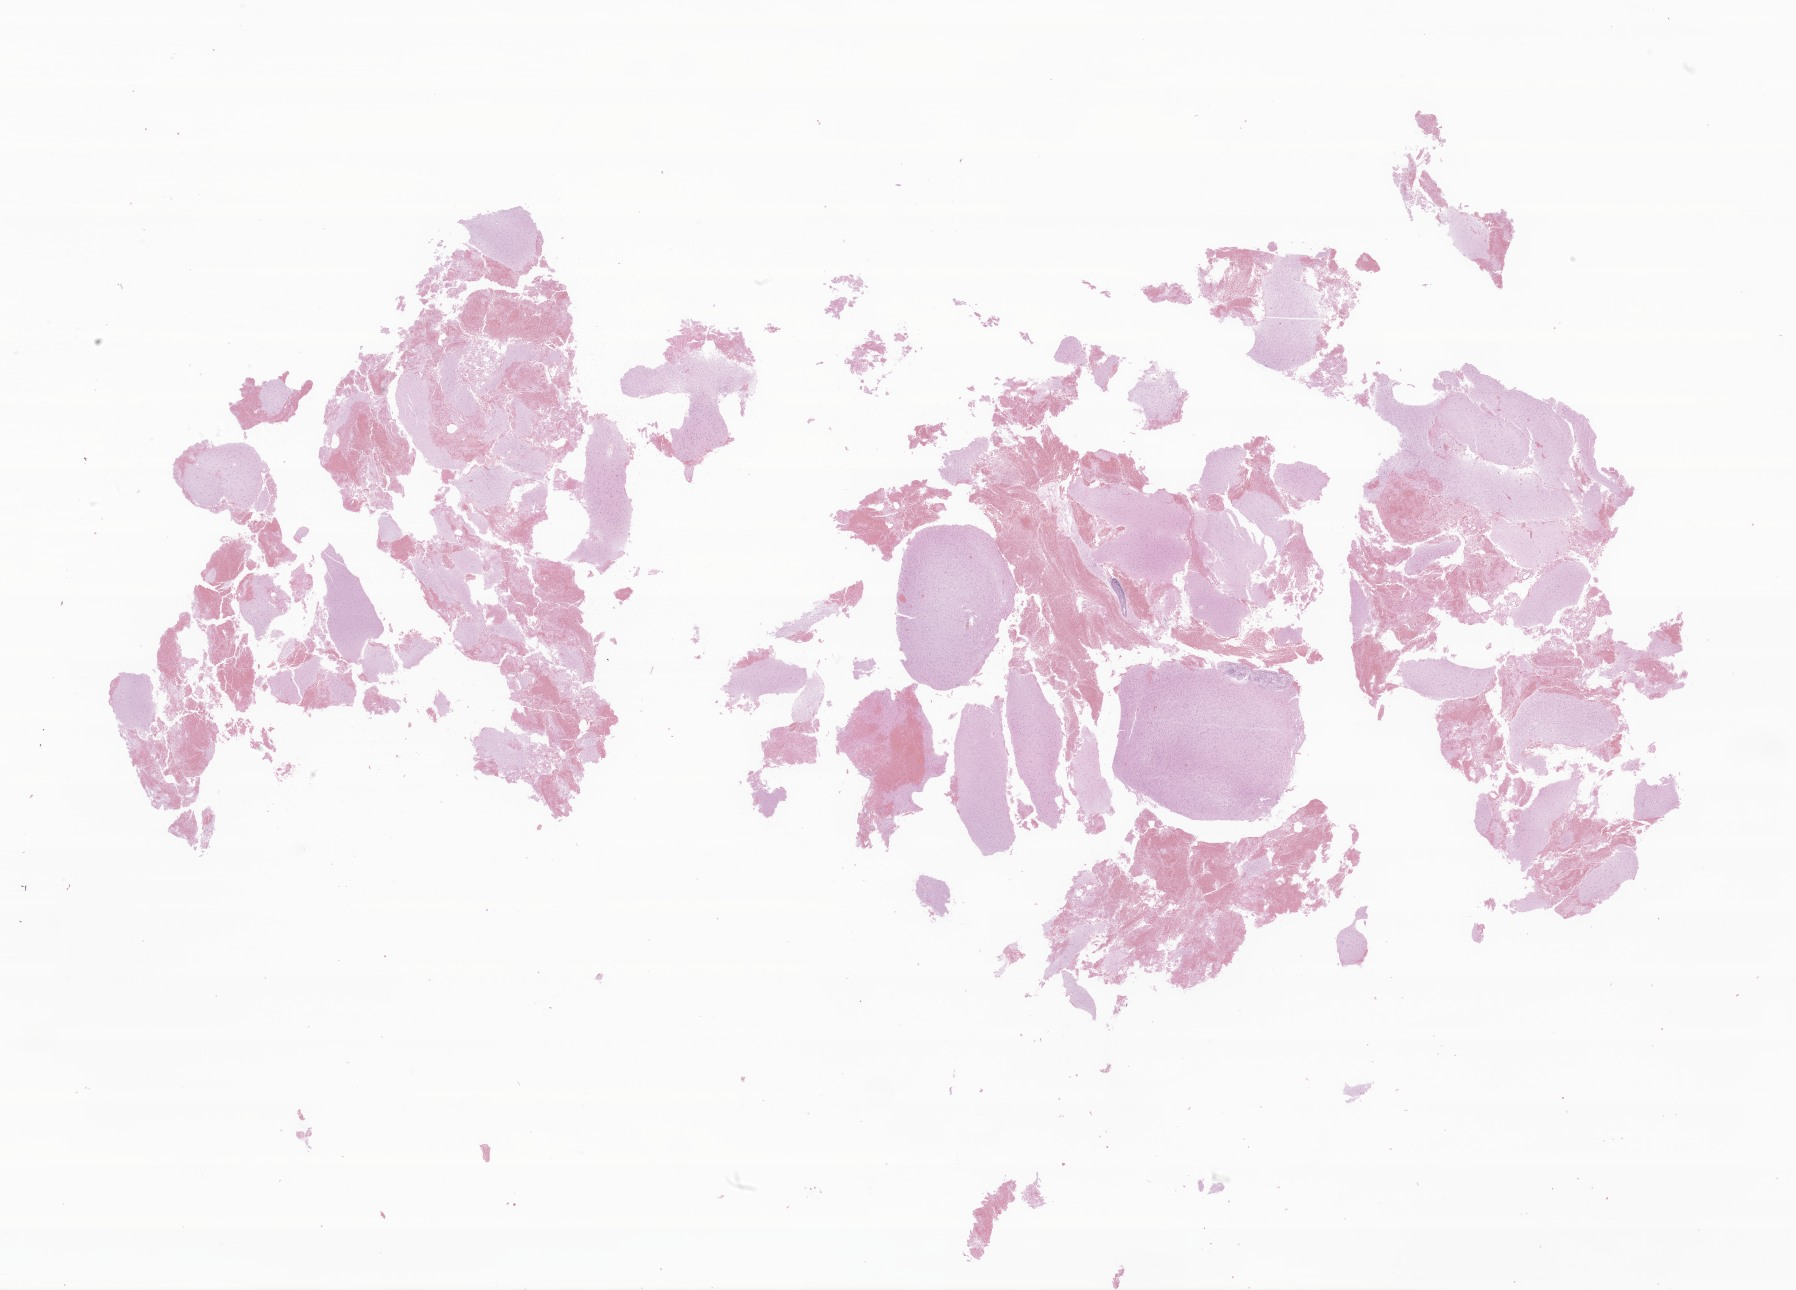
H&E whole-slide image of tumor tissue from the brain, low-resolution overview of the scanned area, about 30.3 x 21.8 mm, formalin-fixed, paraffin-embedded (FFPE) tissue. Male patient, age 231 months (19 years 3 months).
* recorded diagnosis: Neoplasm, uncertain whether benign or malignant